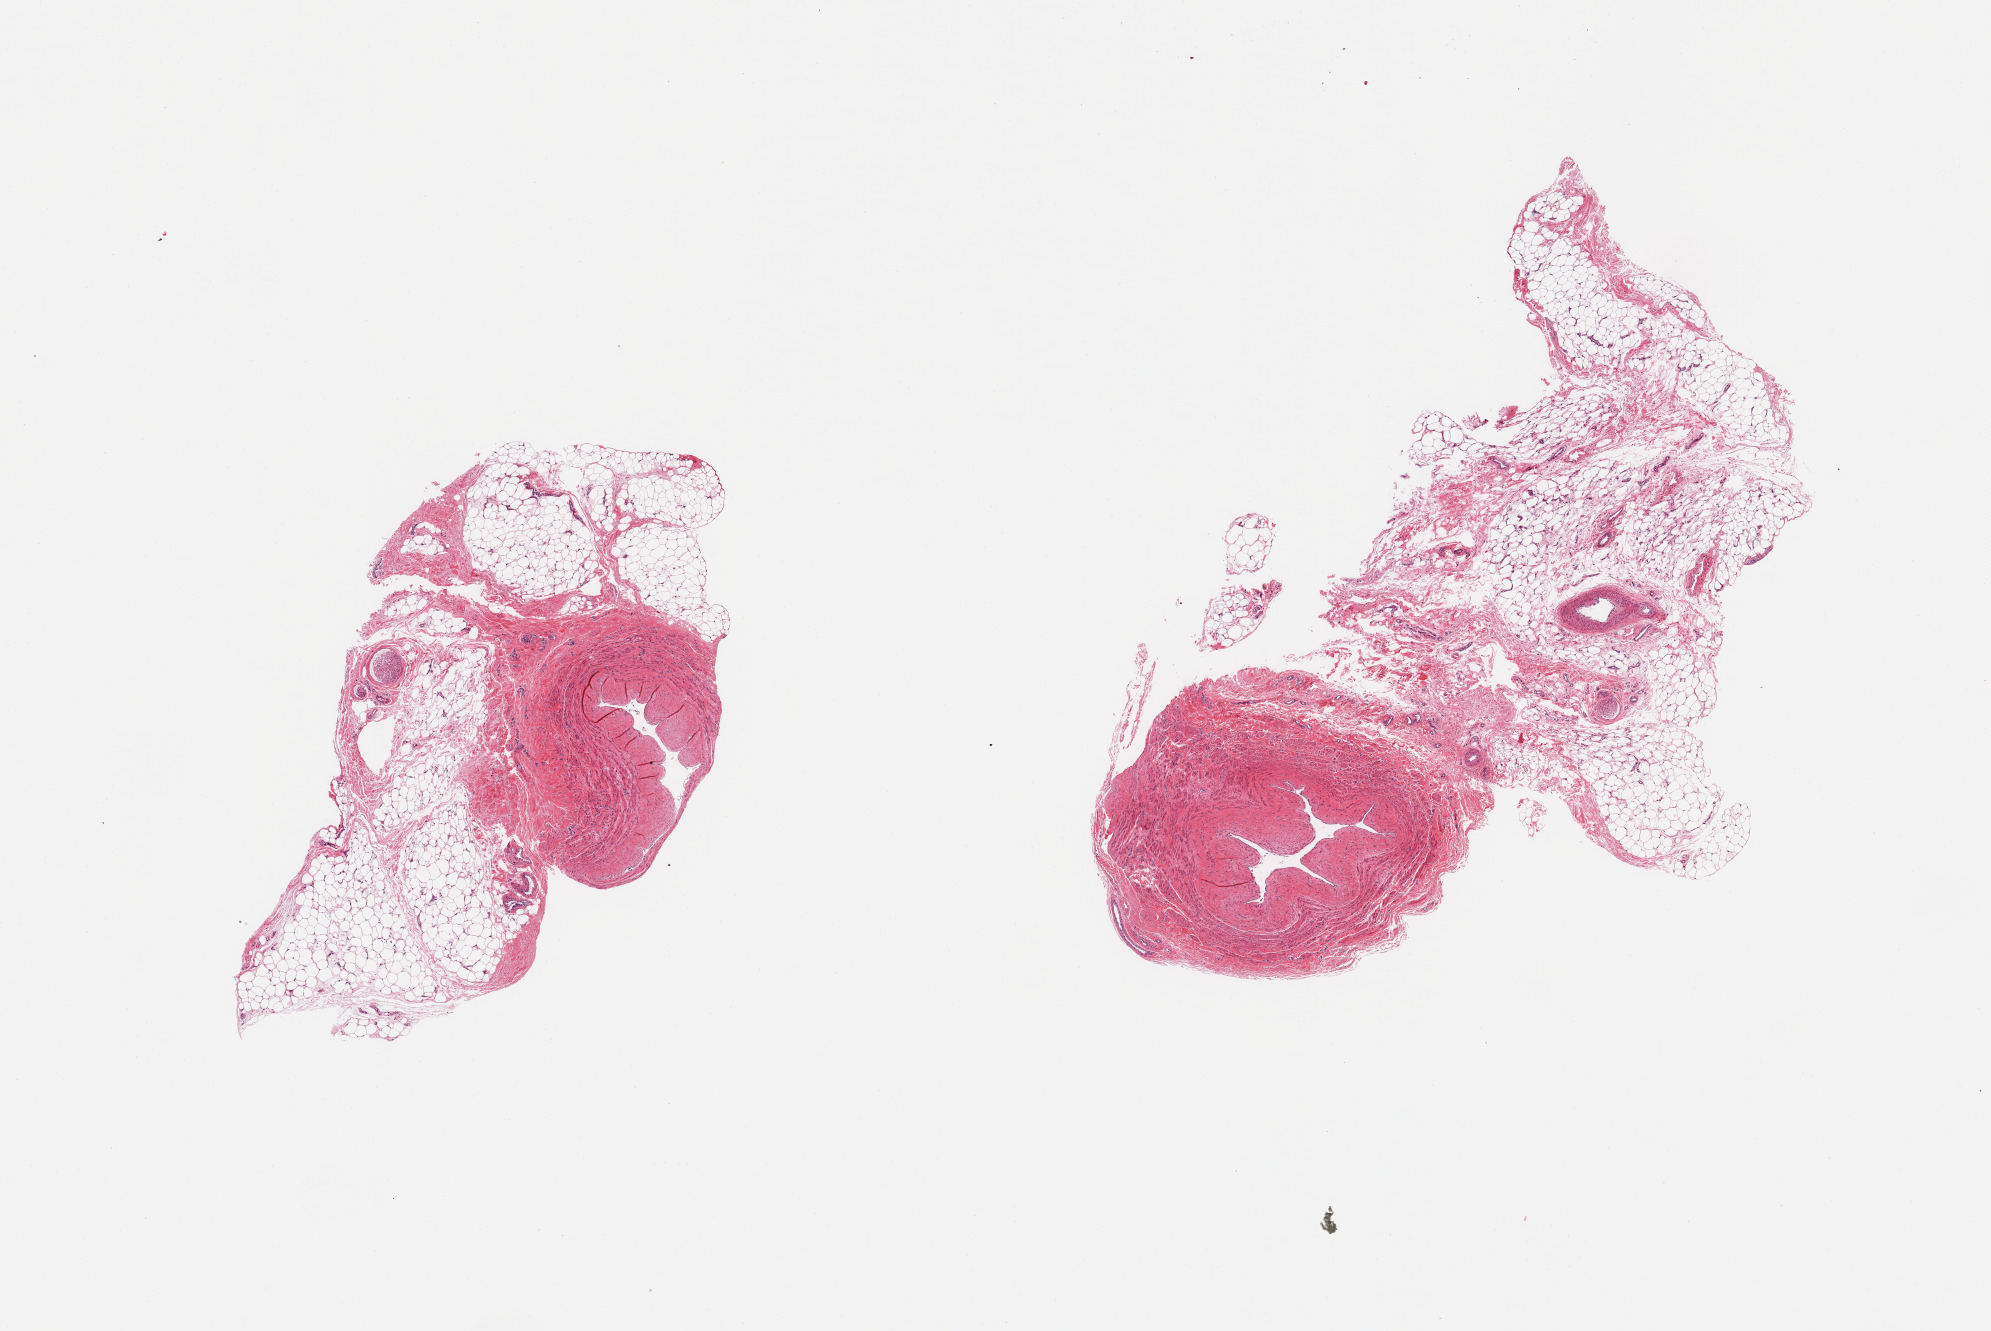
H&E whole-slide image, brightfield — shown as a low-resolution overview of the whole scanned area (about 15.8 x 10.5 mm). PAXgene-fixed, paraffin-embedded tissue. Sampled site (target tissue): tibial artery. Donor tissue sample. Donor: female.
- pathologist's review note for this sample: 2 pieces; significant residual fat (70%)